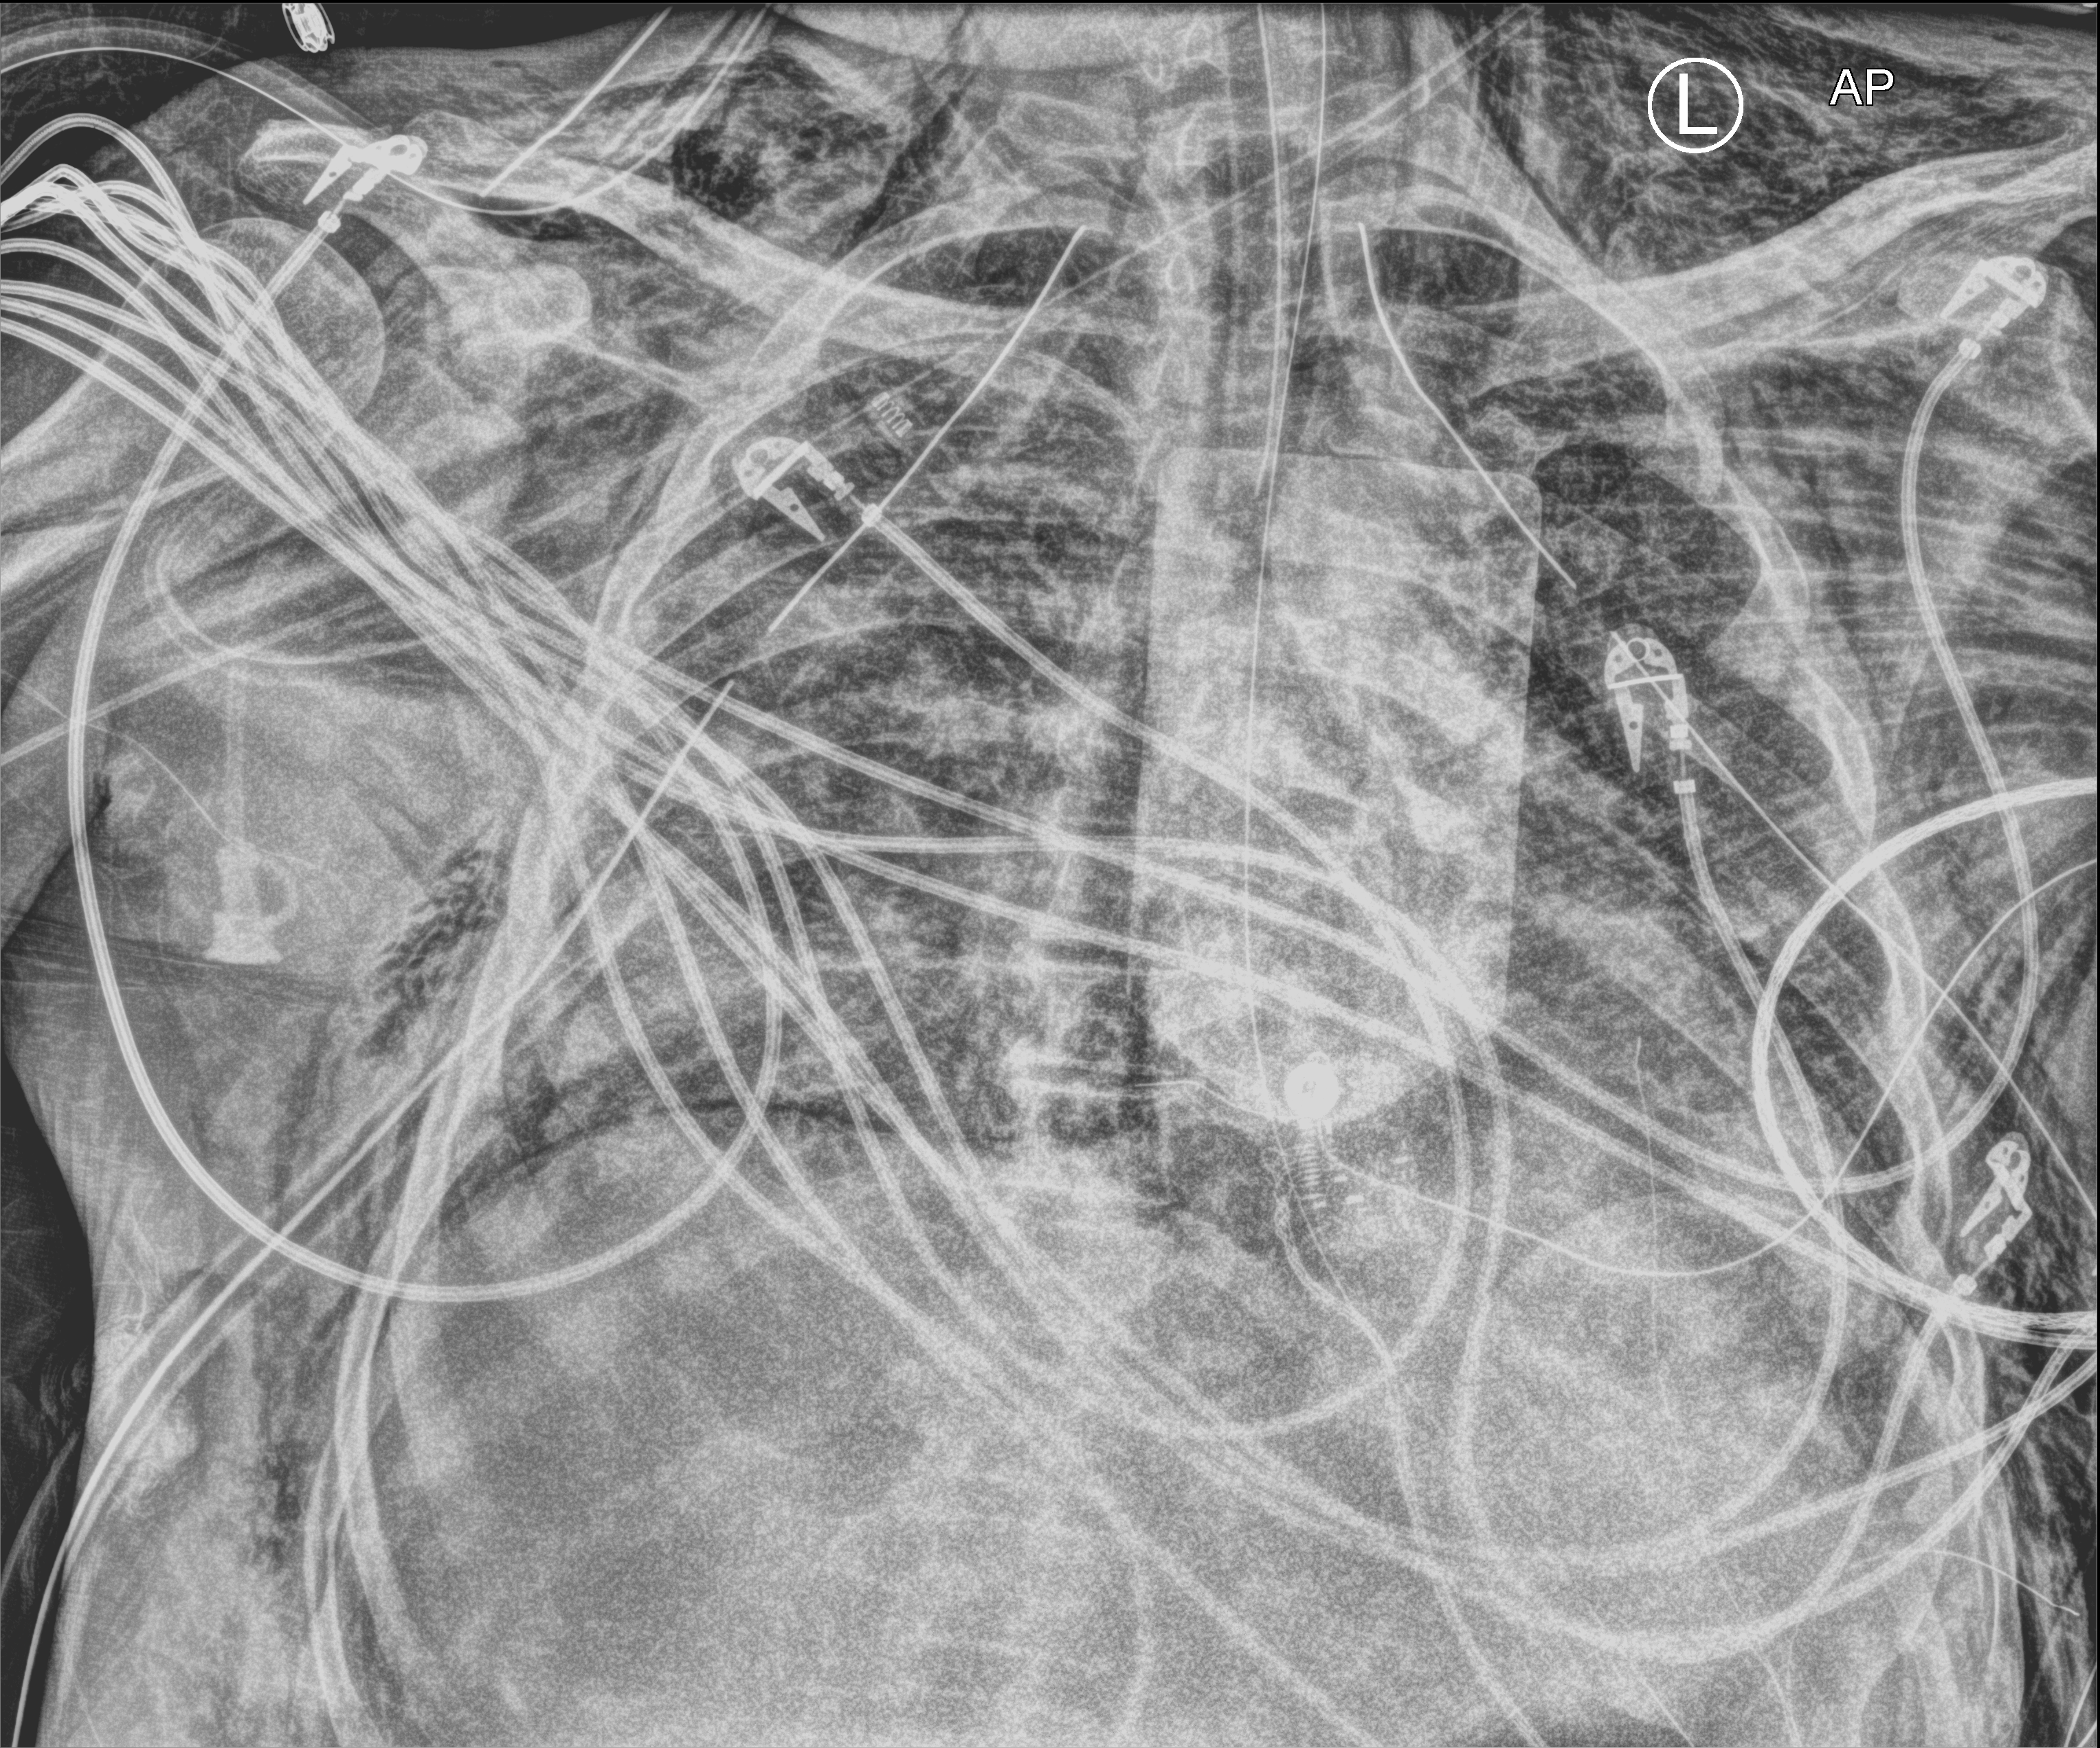
Chest X-ray (portable), anteroposterior (AP) projection. Male patient hospitalised with COVID-19, age 18–59 years.
Hospital-stay facts (about this admission, not read from this image; timing relative to this image not recorded): mechanically ventilated during this hospital stay: yes; length of hospital stay: 83 days.